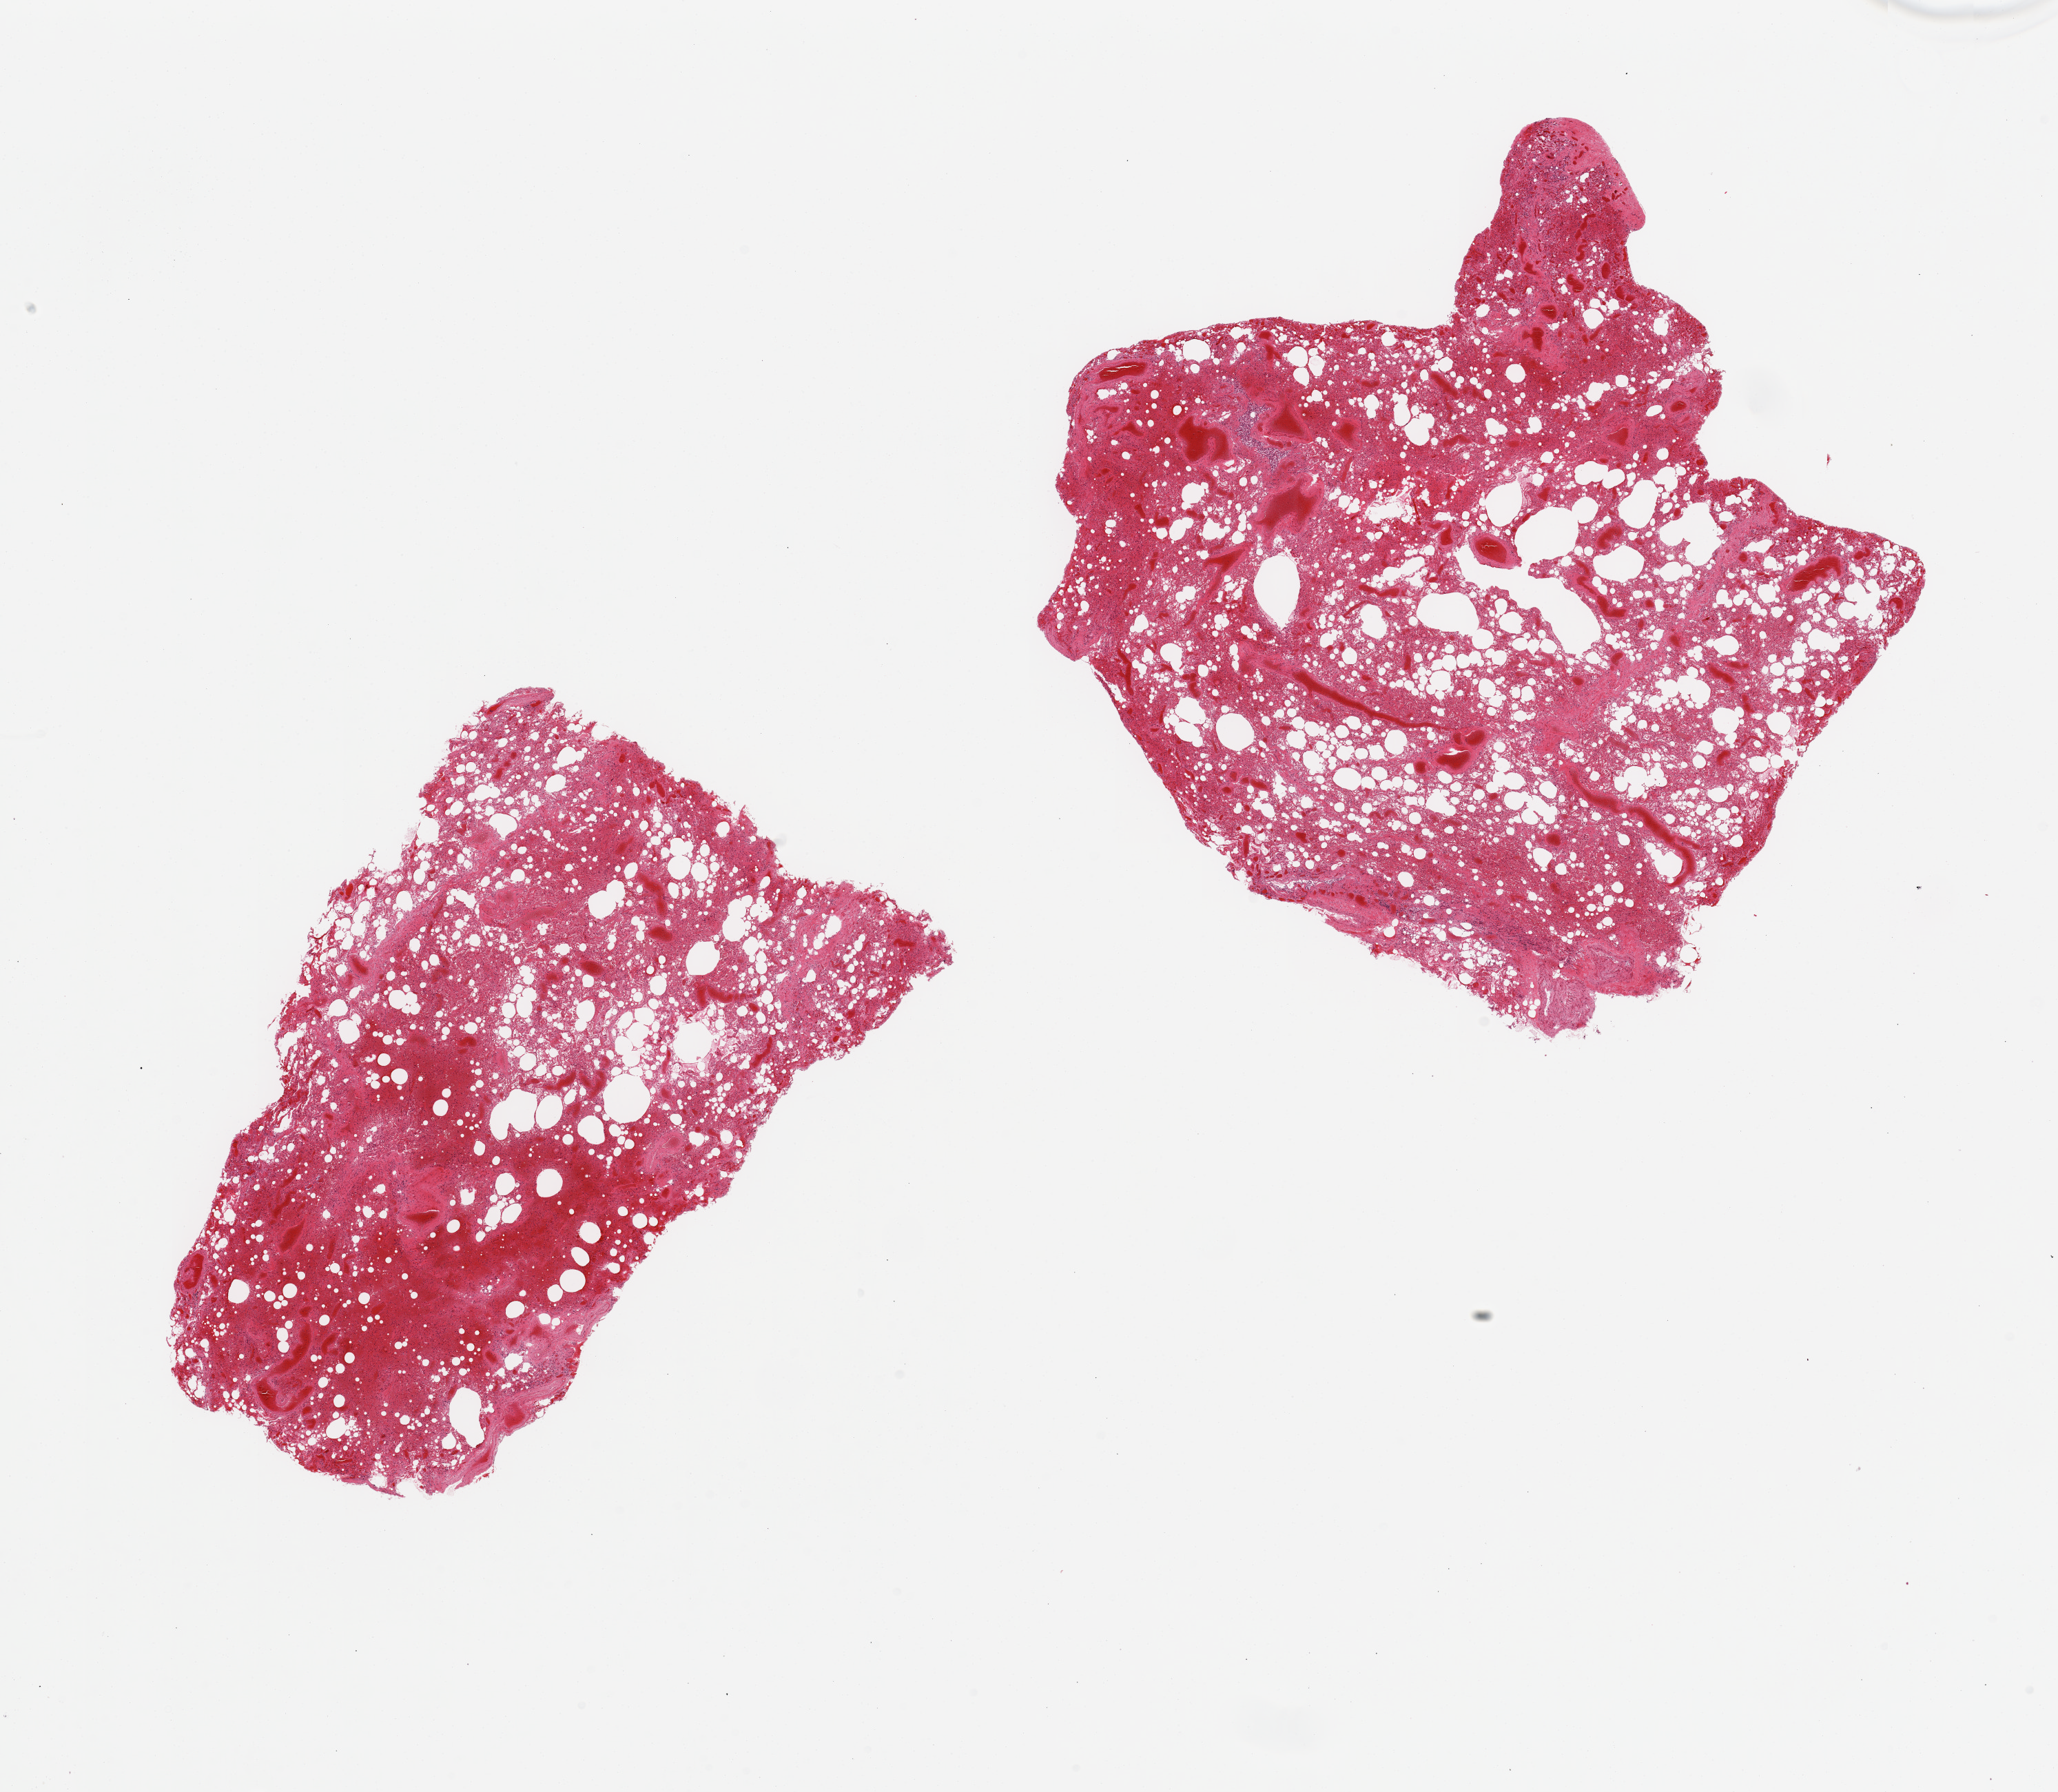
Whole-slide image, haematoxylin and eosin stain — low-resolution overview of the scanned area, about 23.6 x 20.6 mm; PAXgene-fixed paraffin-embedded (PFPE) section; section of lung (target tissue); donor tissue sample. Donor: female.
Reviewer comment on this tissue sample: 2 pieces; emphysema; moderate vascular congestion and patchy alveolar hemorrhage.